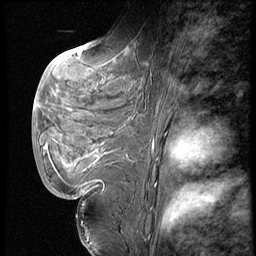
Breast MRI (dynamic contrast-enhanced), one sagittal slice. Slice 26 of 62 in the series (ordered by position). Dynamic contrast-enhanced series, image 2 of 4 at this slice position (ordered by acquisition). 1.5 T. TE 4.2 ms, TR 9 ms. 256 × 256 image matrix. Patient: female, 28 years. Case-level facts recorded for this patient, not image findings: setting: breast cancer imaged before/during neoadjuvant chemotherapy.
Structures marked on this image (semi-automatically segmented with operator editing):
- analysis volume of interest (the breast-tissue region the enhancement analysis was run in; not a lesion): box from (x=40, y=54) to (x=150, y=183) px
- tumour enhancement mask (voxels above the 140 % enhancement threshold inside the analysis volume of interest): (x=87, y=145)–(x=95, y=157)